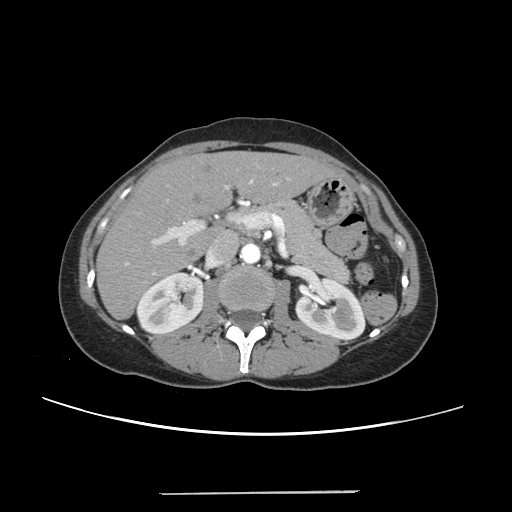
Contrast-enhanced abdominal CT, one axial slice. Position 128 of 240 along the scan axis. Intravenous contrast given. Soft-tissue window (W 400 / L 40 HU). 1.25 mm slice thickness. 512 × 512 image matrix, field of view 371 × 371 mm. Female patient, age 60 years. Case-level facts recorded for this patient, not image findings: diagnosis: colorectal cancer liver metastases, imaged before liver resection; multiple liver metastases: no; largest metastasis: 1.5 cm.
Annotated regions visible in this slice (manually delineated by an expert):
- liver: bounding box <98,152,332,318> (left, top, right, bottom; pixels)
- planned liver remnant (the part of the liver to remain after resection): <98,152,332,318>
- portal vein (with intrahepatic branches): <125,177,289,275>
- liver metastasis: <203,164,213,173>